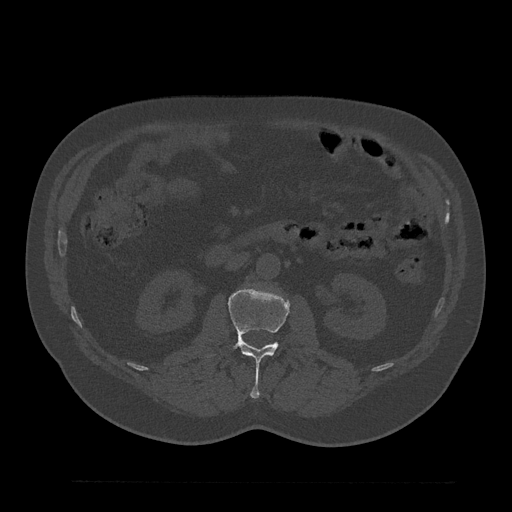
CT including the spine, one axial slice. Position 94 of 797 along the scan axis. Reconstruction kernel Br40s/3. 120 kVp. Bone window (W 1800 / L 400 HU). 512 × 512 image matrix, field of view 430 × 430 mm. Male patient, age 61 years. From the clinical record (not read from this slice): primary cancer: prostate.
Annotated regions visible in this slice (semi-automatic segmentation, software-assisted and operator-edited):
- L2 vertebra: bounding box [x1, y1, x2, y2] px = [206, 286, 289, 398]